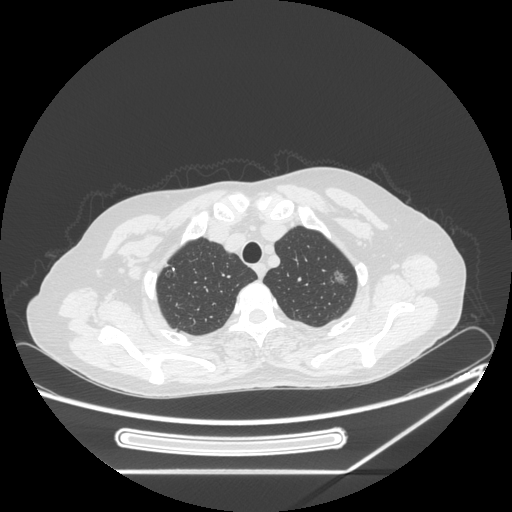
Chest CT, one axial slice. Position 206 of 250 along the scan axis. 120 kVp. Lung window (W 1500 / L -600 HU). 1.25 mm slice thickness. 512 × 512 image matrix, field of view 409 × 409 mm. Patient: female, 57 years. From the clinical record (not read from this slice): clinical TNM (as recorded): T1c N0 M0; histopathological grade: G2-3.
Structures marked on this image (rectangle marked by the reading radiologist):
- lung tumour (recorded histology: adenocarcinoma): bounding box <326,268,353,295> (left, top, right, bottom; pixels)